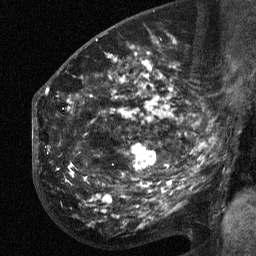
Breast MRI (dynamic contrast-enhanced), one sagittal slice; slice 34 of 64 in the series (ordered by position); dynamic contrast-enhanced study with each time point stored as its own series, time point 2 of 3 at this slice position (early post-contrast, ordered by acquisition time); 1.5 T; TE 4.8 ms, TR 27 ms; 2.3 mm slice thickness; 256 × 256 image matrix. Patient: female, 50 years. Case-level facts recorded for this patient, not image findings: setting: breast cancer imaged before/during neoadjuvant chemotherapy; receptor status: HER2-positive.
Structures marked on this image (semi-automatic segmentation, software-assisted and operator-edited):
- analysis volume of interest (the breast-tissue region the enhancement analysis was run in; not a lesion): bounding box (x1, y1, x2, y2) in pixels: (53, 64, 211, 213)
- tumour enhancement mask (voxels above the 90 % enhancement threshold inside the analysis volume of interest): (120, 67, 154, 169)